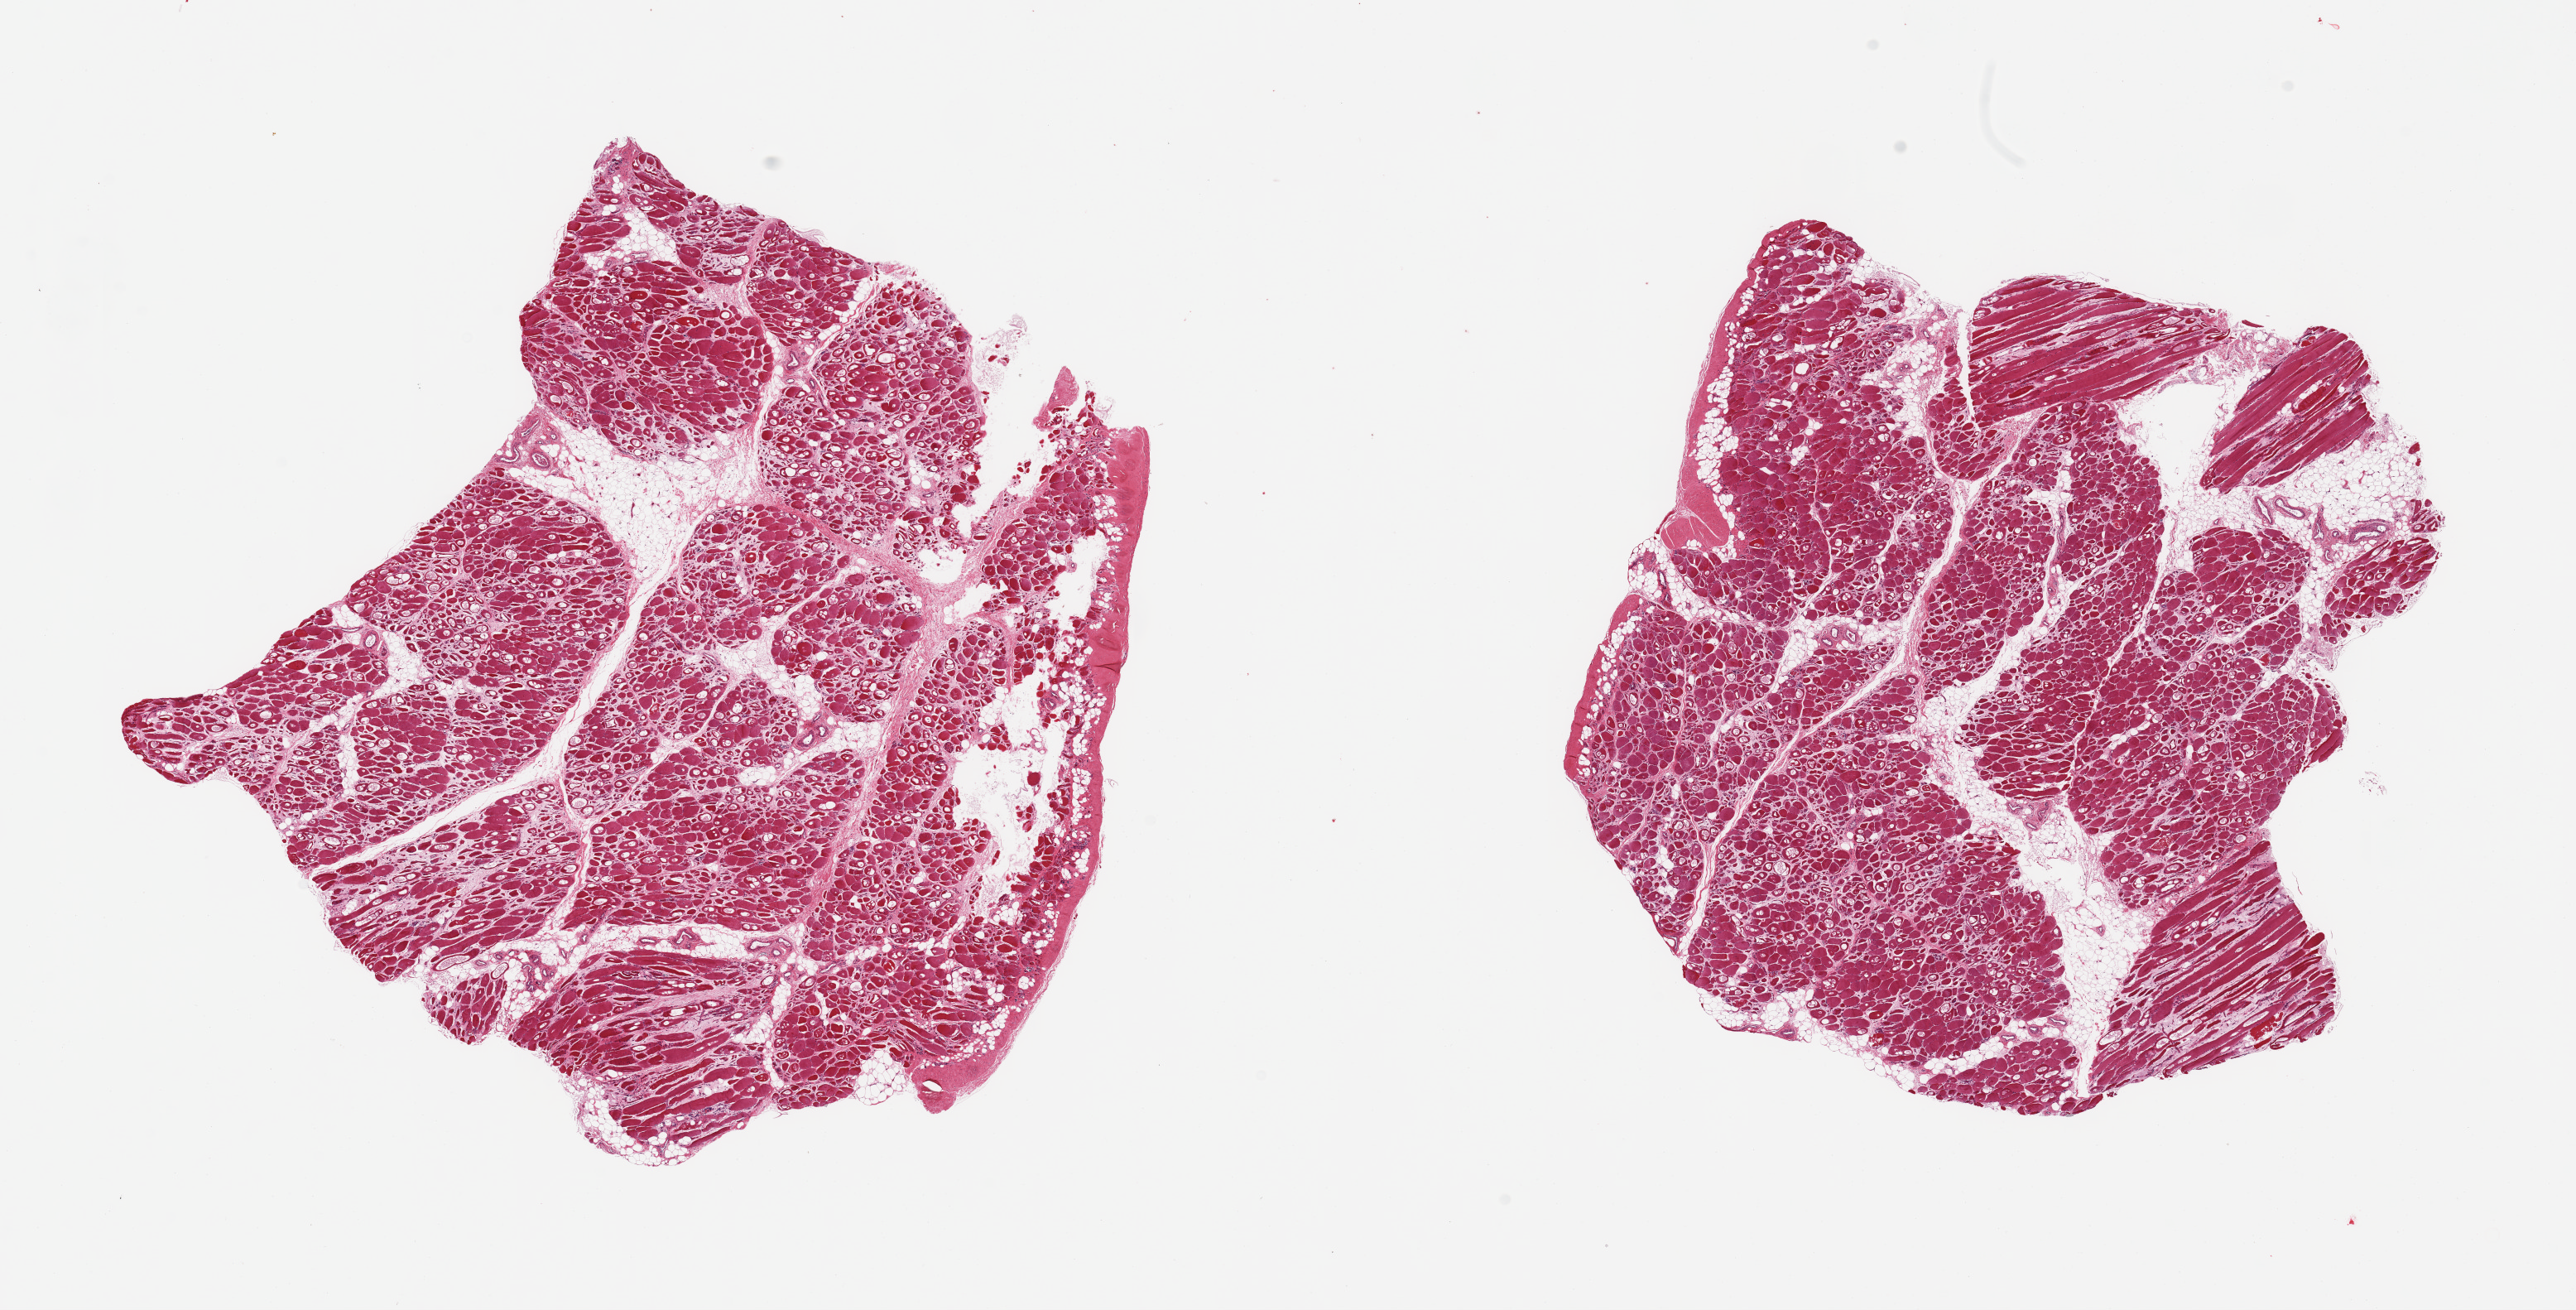
H&E whole-slide image, whole scanned area (about 24.6 x 12.5 mm) shown as a low-resolution overview. PAXgene-fixed paraffin-embedded (PFPE) section. Section of skeletal muscle (target tissue). Tissue donor sample. Donor: male.
Pathologist's review note for this sample: 2 pieces, moderate atrophy.